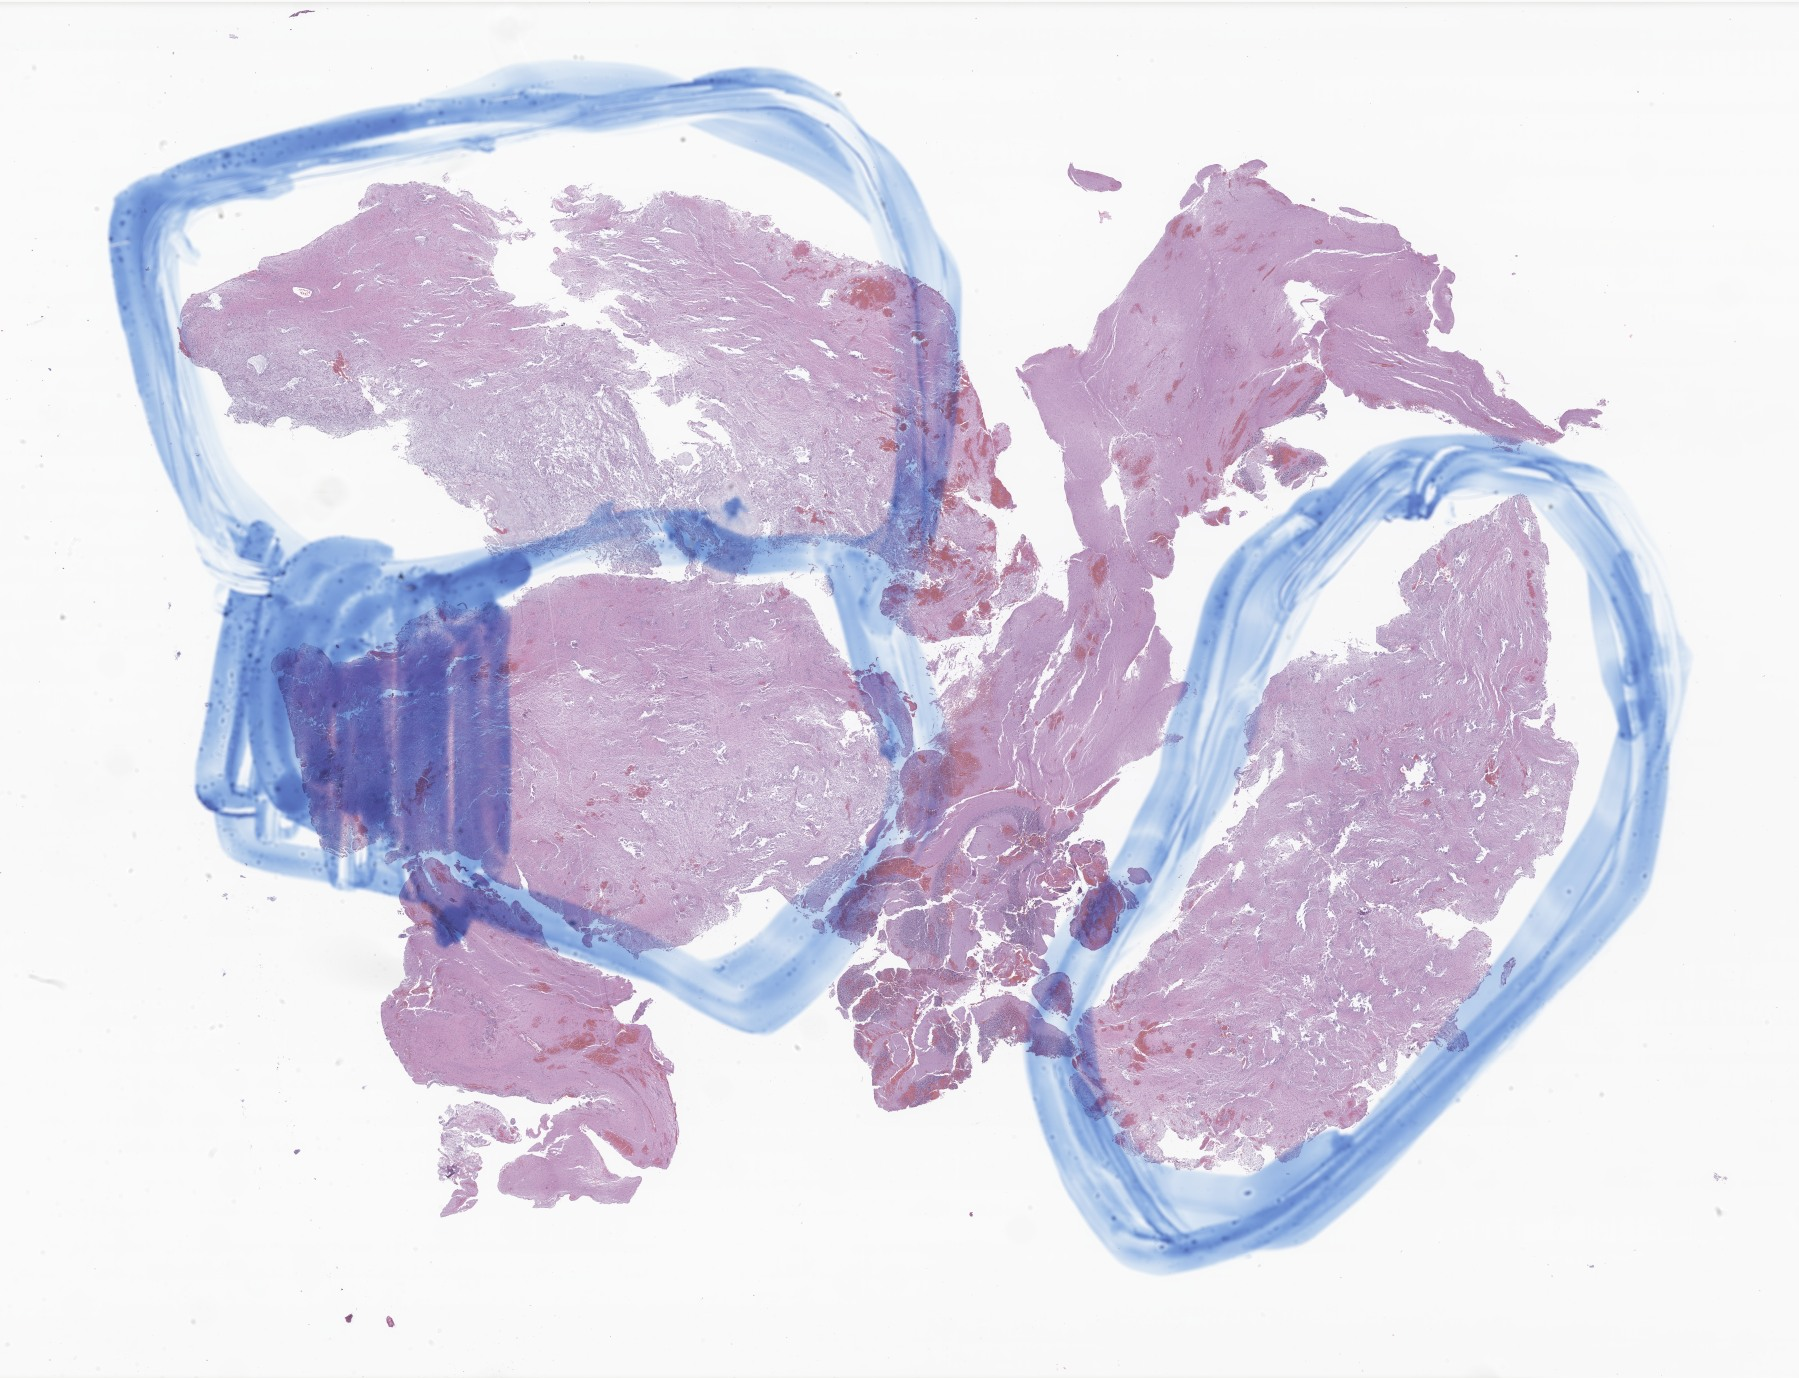
Digitized H&E-stained section of tumor tissue from the brain, low-resolution overview of the scanned area, about 30.3 x 23.2 mm. FFPE section. Patient female; age 146 months (12 years 2 months).
• diagnosis: Pilocytic astrocytoma